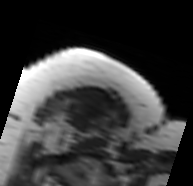
MRI of an extremity soft-tissue mass, one axial slice. Slice 63 of 91 in the series (ordered by position). MR volume resampled by the dataset authors to the PET/CT grid (not the native acquisition matrix). 3.27 mm slice thickness. 193 × 186 image matrix, field of view 188 × 182 mm. Female patient. Case-level facts recorded for this patient, not image findings: histological type: malignant solitary fibrous tumor; grade: intermediate; site of the primary tumour: right thigh.
Structures marked on this image (expert contour drawn on MRI and transferred to this co-registered scan by the dataset authors):
- gross tumour volume including surrounding oedema: bounding box (x1, y1, x2, y2) in pixels: (47, 97, 118, 150)
- gross tumour volume (mass): (69, 101, 102, 132)